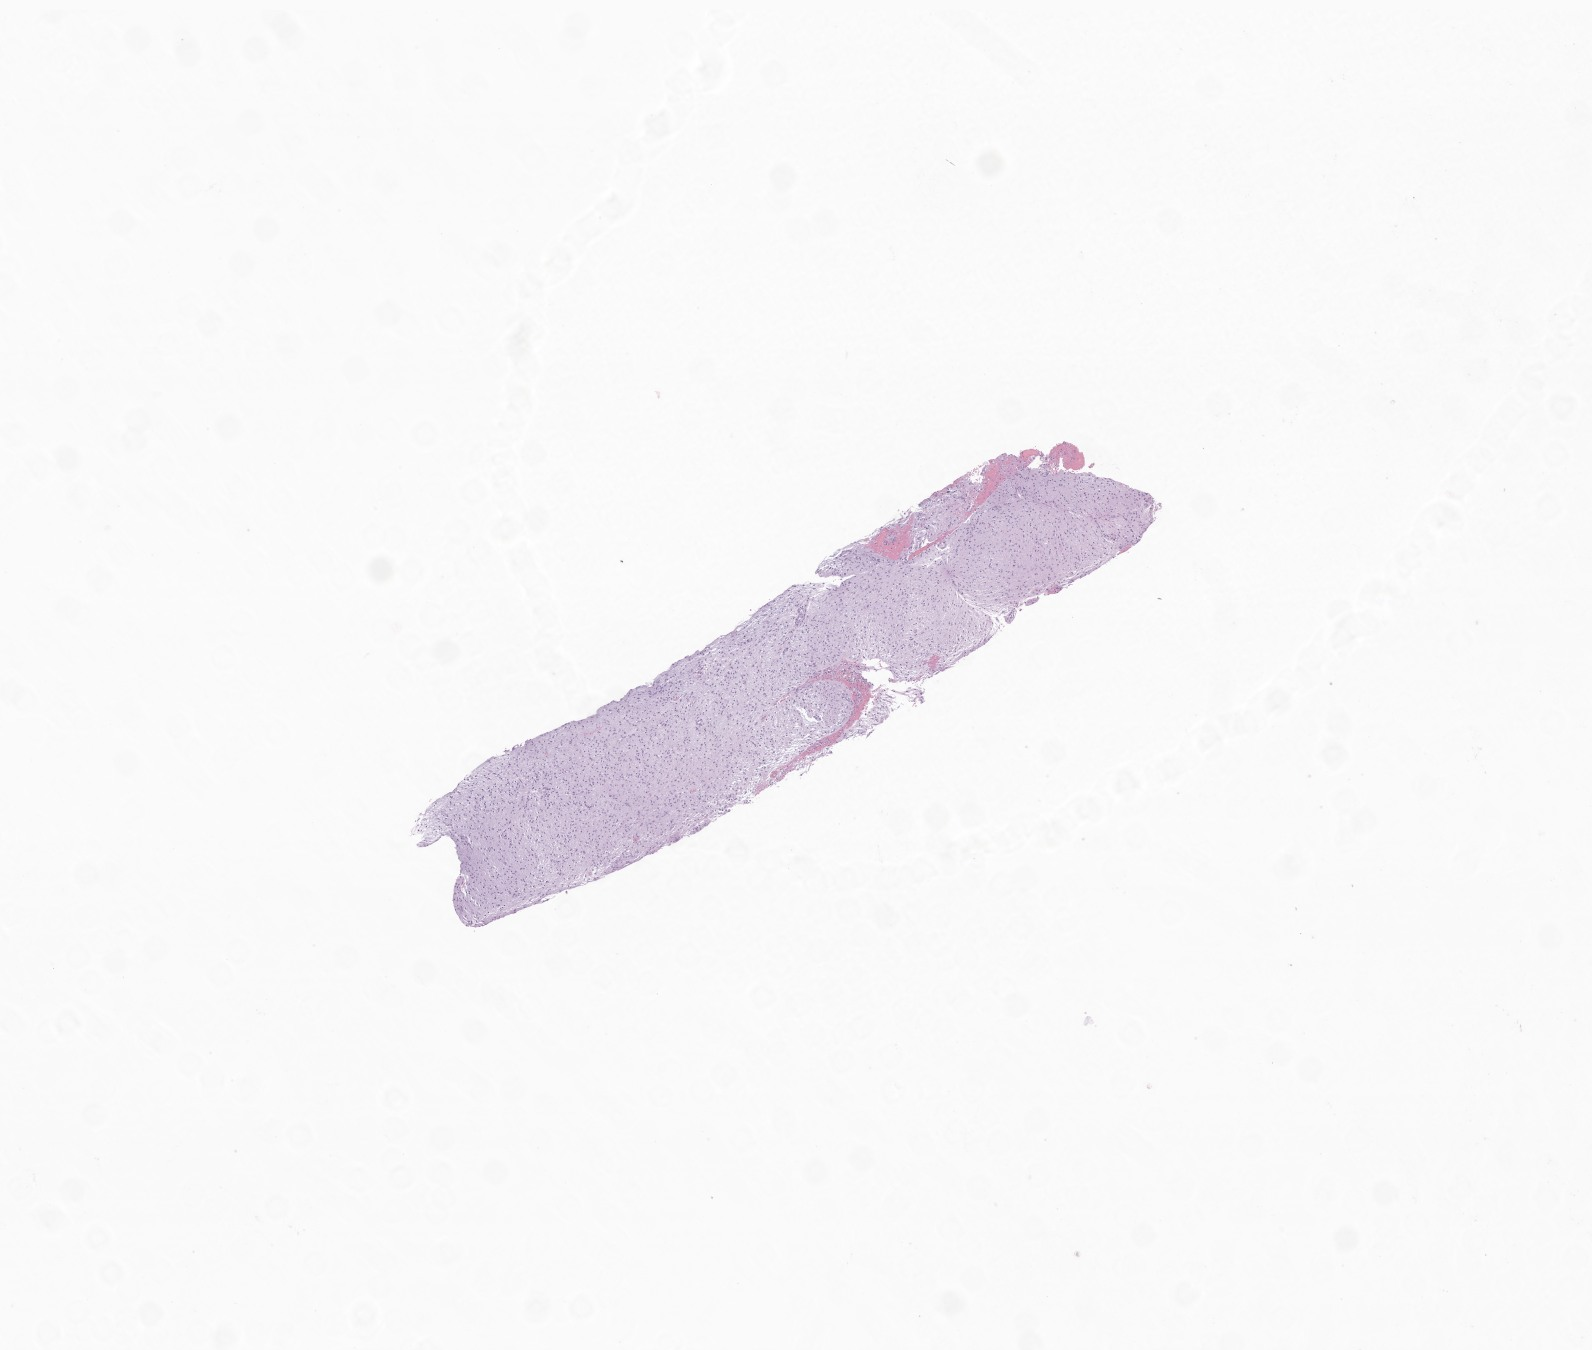
Whole-slide image, hematoxylin and eosin (H&E) stain of tumor tissue from the brain — low-resolution overview of the scanned area, about 6.7 x 5.7 mm; formalin-fixed paraffin-embedded section. Male patient, age 148 months (12 years 4 months).
- diagnosis (ICD-O-3 morphology term): Dysembryoplastic neuroepithelial tumor